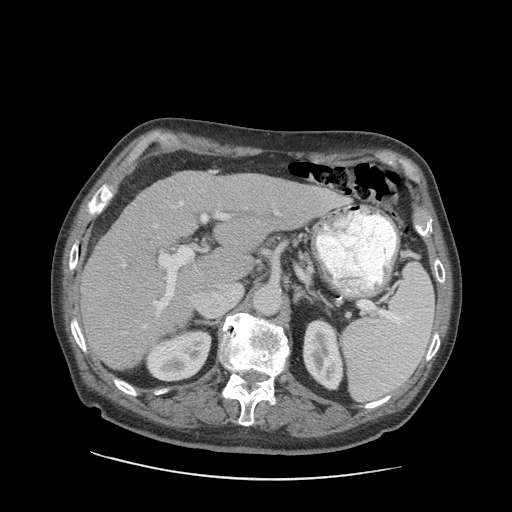
Contrast-enhanced abdominal CT (liver protocol), one axial slice. Slice 54 of 89 in the series (ordered by position). Soft-tissue window (W 400 / L 40 HU). 2.5 mm slice thickness. 512 × 512 image matrix. Case-level facts recorded for this patient, not image findings: diagnosis: hepatocellular carcinoma (patient treated with transarterial chemoembolisation; whether this scan precedes or follows treatment is not stated here); TNM stage (as recorded): Stage-I.
Annotated regions visible in this slice (semi-automatic segmentation, software-assisted and operator-edited):
- liver parenchyma outside the tumour (the mass and vessels are separate outlines, so this box may not span the whole liver): bounding box [x1, y1, x2, y2] px = [80, 170, 342, 370]
- liver vessels: [122, 171, 341, 334]